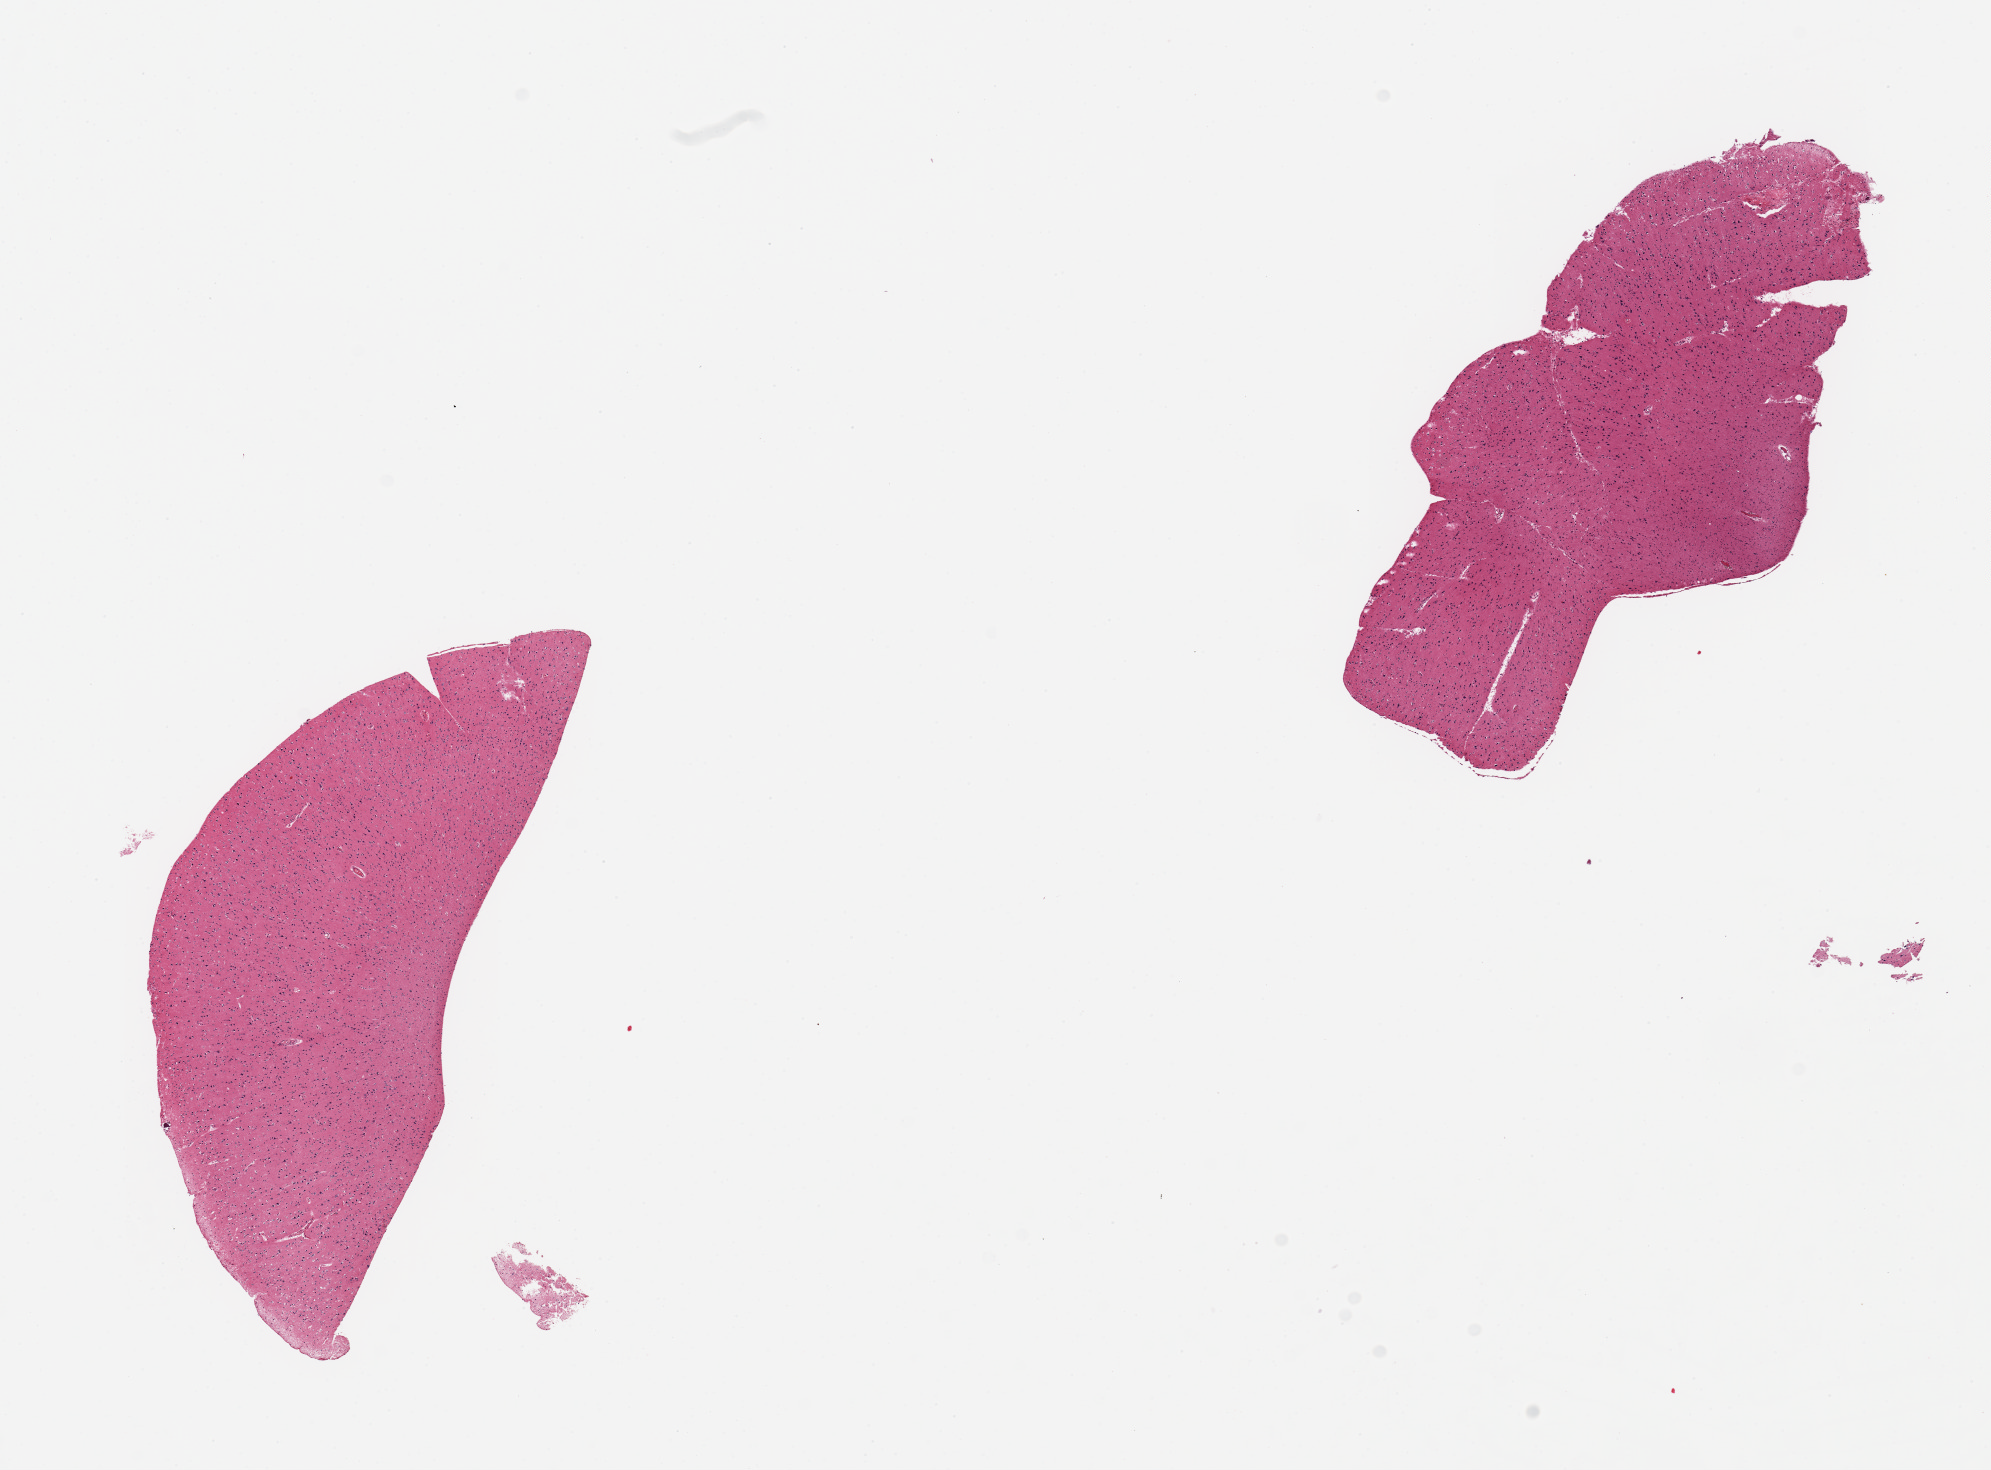
Whole-slide image, hematoxylin and eosin (H&E) stain — low-resolution overview of the scanned area, about 15.8 x 11.6 mm; PAXgene-fixed paraffin-embedded (PFPE) section; target tissue: cerebral cortex; donor tissue sample. Donor sex: male.
Review note (as recorded): 2 pieces, no abnormalities noted.